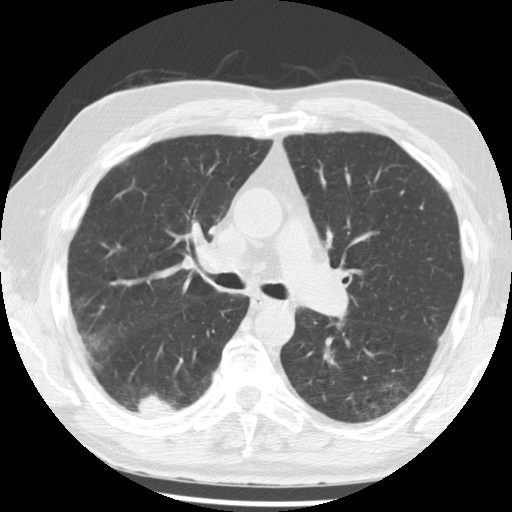
Chest CT (low-dose screening protocol), one axial image, third annual screen, lung window (W 1500 / L -600 HU), 2.5 mm slice thickness, standard (soft-tissue) reconstruction kernel (STANDARD), slice 127 of 221 in the series, 512 × 512 image matrix. Male participant, aged 68 years at enrolment. Current smoker at enrolment.
- Lesion marked by an expert reader, box from (x=119, y=378) to (x=192, y=431) px.
- The screening reader recorded 3 non-calcified nodules or masses ≥4 mm on this exam (right lower lobe, right lower lobe, right lower lobe); which of them this box marks is not recorded.
- Participant outcome: lung cancer diagnosed 48 days after this screen — squamous cell carcinoma, NOS, right lower lobe, moderately differentiated (G2), stage IB (AJCC 6th edition), 20 mm at pathology.